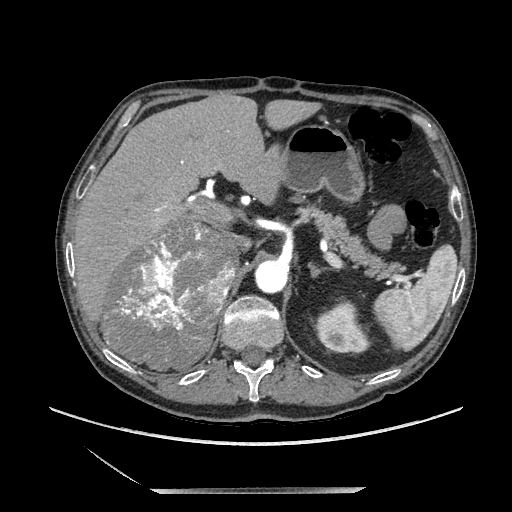
Contrast-enhanced abdominal CT, one axial slice; slice 140 of 243 in the series (ordered by position); soft-tissue window (W 400 / L 40 HU); 1.25 mm slice thickness; 512 × 512 image matrix, field of view 420 × 420 mm. Male patient. From the clinical record (not read from this slice): diagnosis: adrenocortical carcinoma; tumour side: right adrenal; tumour size at pathology: 16 cm; Ki-67 index: 17 %; stage (as recorded): 3.
Annotated regions visible in this slice (semi-automatic segmentation, software-assisted and operator-edited):
- mass: box from (x=107, y=223) to (x=236, y=368) px